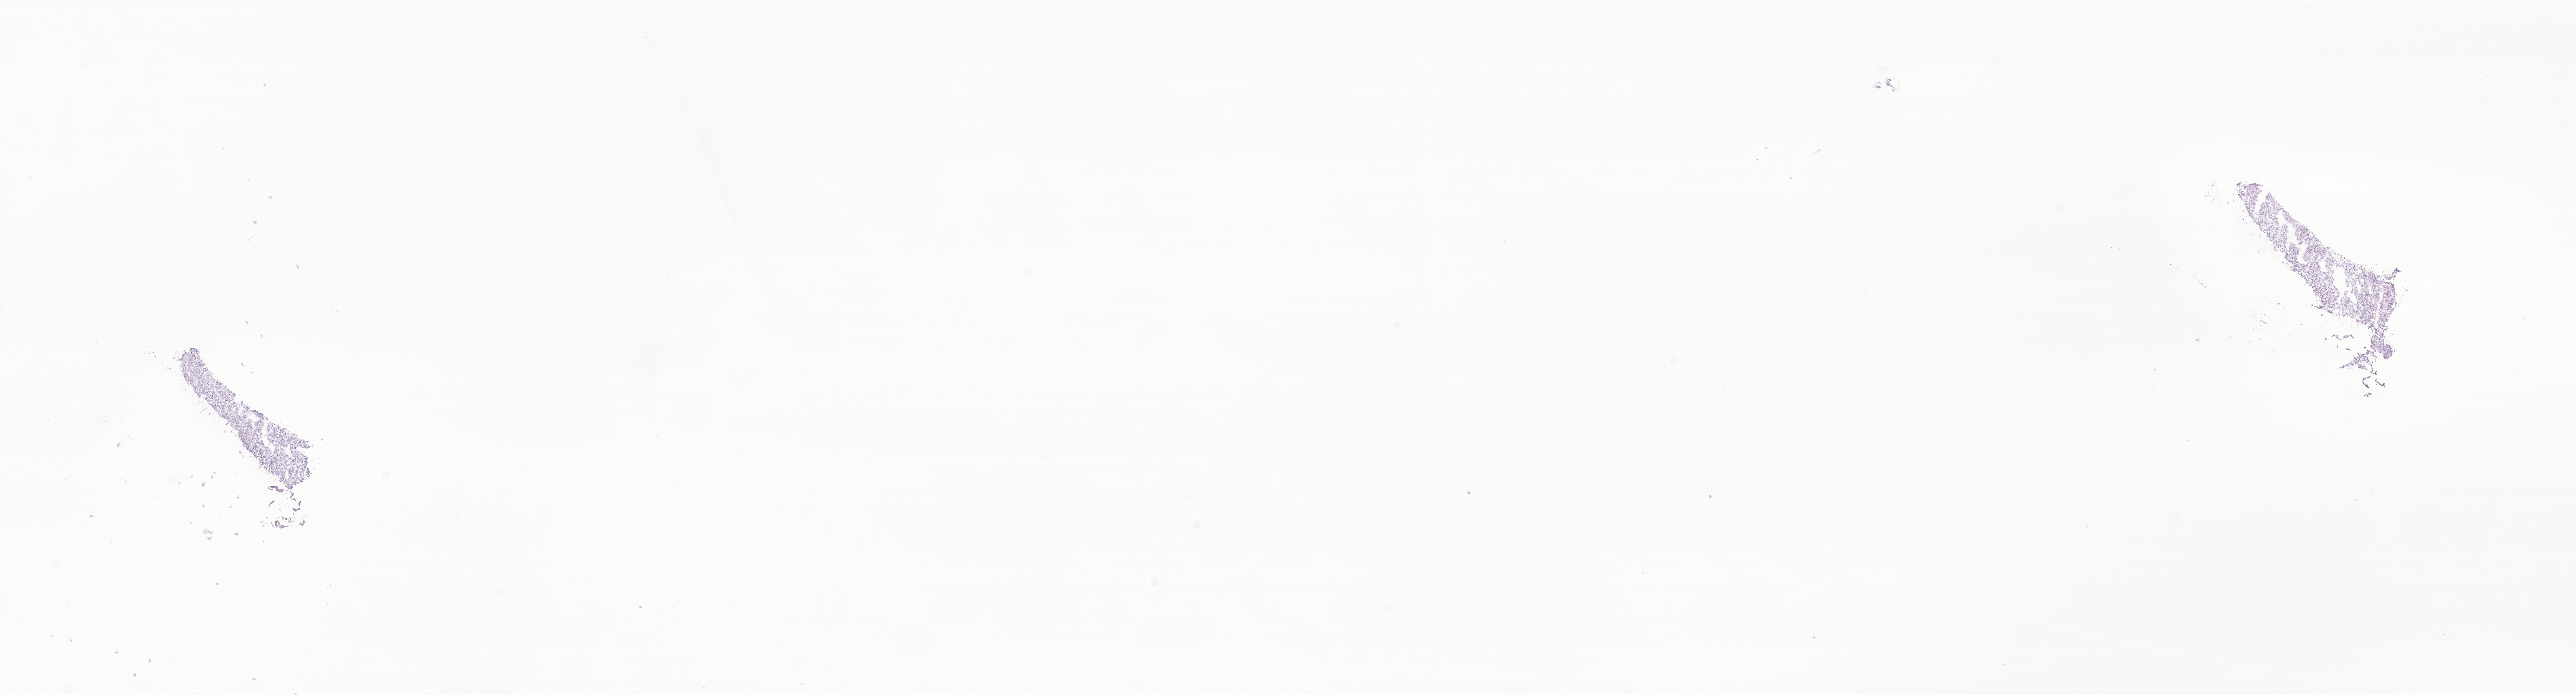
Haematoxylin and eosin whole-slide image of tumor tissue from the cerebellum, a low-resolution overview of the entire scanned area, about 28.3 x 7.6 mm; cryosection (OCT / tissue freezing medium). Patient: female, age 676 days (about 1.9 years).
Recorded diagnosis: Neoplasm, uncertain whether benign or malignant.